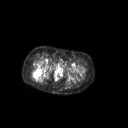
FDG PET of an extremity soft-tissue mass (from a PET/CT study), one axial slice. Position 59 of 267 along the scan axis. 3.27 mm slice thickness. 128 × 128 image matrix. Female patient, age 70 years. Case-level facts recorded for this patient, not image findings: histological type: synovial sarcoma; grade: intermediate; site of the primary tumour: right buttock.
Structures marked on this image (expert contour drawn on MRI and transferred to this co-registered scan by the dataset authors):
- gross tumour volume including surrounding oedema: bounding box <32,67,45,81> (left, top, right, bottom; pixels)
- gross tumour volume (mass): <32,67,43,77>